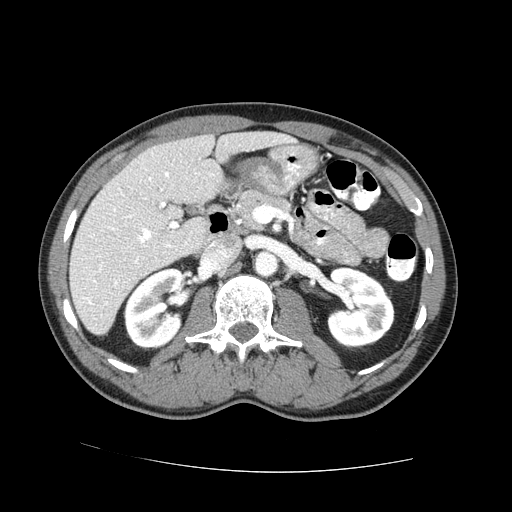
Contrast-enhanced abdominal CT (liver protocol), one axial slice. Slice 32 of 73 in the series (ordered by position). Reconstruction kernel STANDARD. One of 2 acquisitions stored at this slice position. Soft-tissue window (W 400 / L 40 HU). 2.5 mm slice thickness. 512 × 512 image matrix, field of view 380 × 380 mm. Case-level facts recorded for this patient, not image findings: diagnosis: hepatocellular carcinoma (patient treated with transarterial chemoembolisation; whether this scan precedes or follows treatment is not stated here); TNM stage (as recorded): Stage-IVA; Child-Pugh class: A; tumour differentiation: no biopsy.
Outlined on this slice (semi-automatic segmentation, software-assisted and operator-edited):
- liver parenchyma outside the tumour (the mass and vessels are separate outlines, so this box may not span the whole liver): bounding box [x1, y1, x2, y2] px = [70, 132, 298, 334]
- liver vessels: [83, 153, 213, 305]